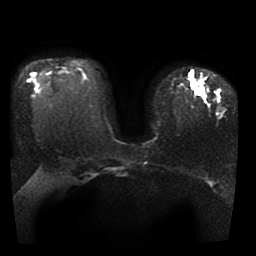
Breast MRI, one axial slice. Position 27 of 41 along the scan axis. Diffusion-weighted series; image 2 of 4 stored at this slice position (different b-values; order by instance number). 1.5 T. 5 mm slice thickness. 256 × 256 image matrix, field of view 330 × 330 mm. Female patient.
Structures marked on this image (outlined manually by an expert reader):
- tumour on diffusion-weighted imaging: bounding box [x1, y1, x2, y2] px = [188, 73, 203, 95]